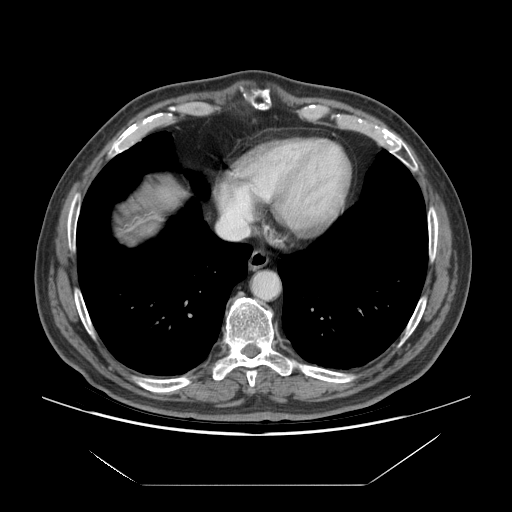
Contrast-enhanced abdominal CT (liver protocol), one axial slice; slice 68 of 75 in the series (ordered by position); reconstruction kernel STANDARD; soft-tissue window (W 400 / L 40 HU); 2.5 mm slice thickness; 512 × 512 image matrix, field of view 420 × 420 mm. From the clinical record (not read from this slice): diagnosis: hepatocellular carcinoma (patient treated with transarterial chemoembolisation; whether this scan precedes or follows treatment is not stated here); TNM stage (as recorded): Stage-I; Child-Pugh class: A; tumour differentiation: well differentiated; tumour nodularity: uninodular.
Annotated regions visible in this slice (semi-automatically segmented with operator editing):
- liver parenchyma outside the tumour (the mass and vessels are separate outlines, so this box may not span the whole liver): bounding box <126,184,180,236> (left, top, right, bottom; pixels)